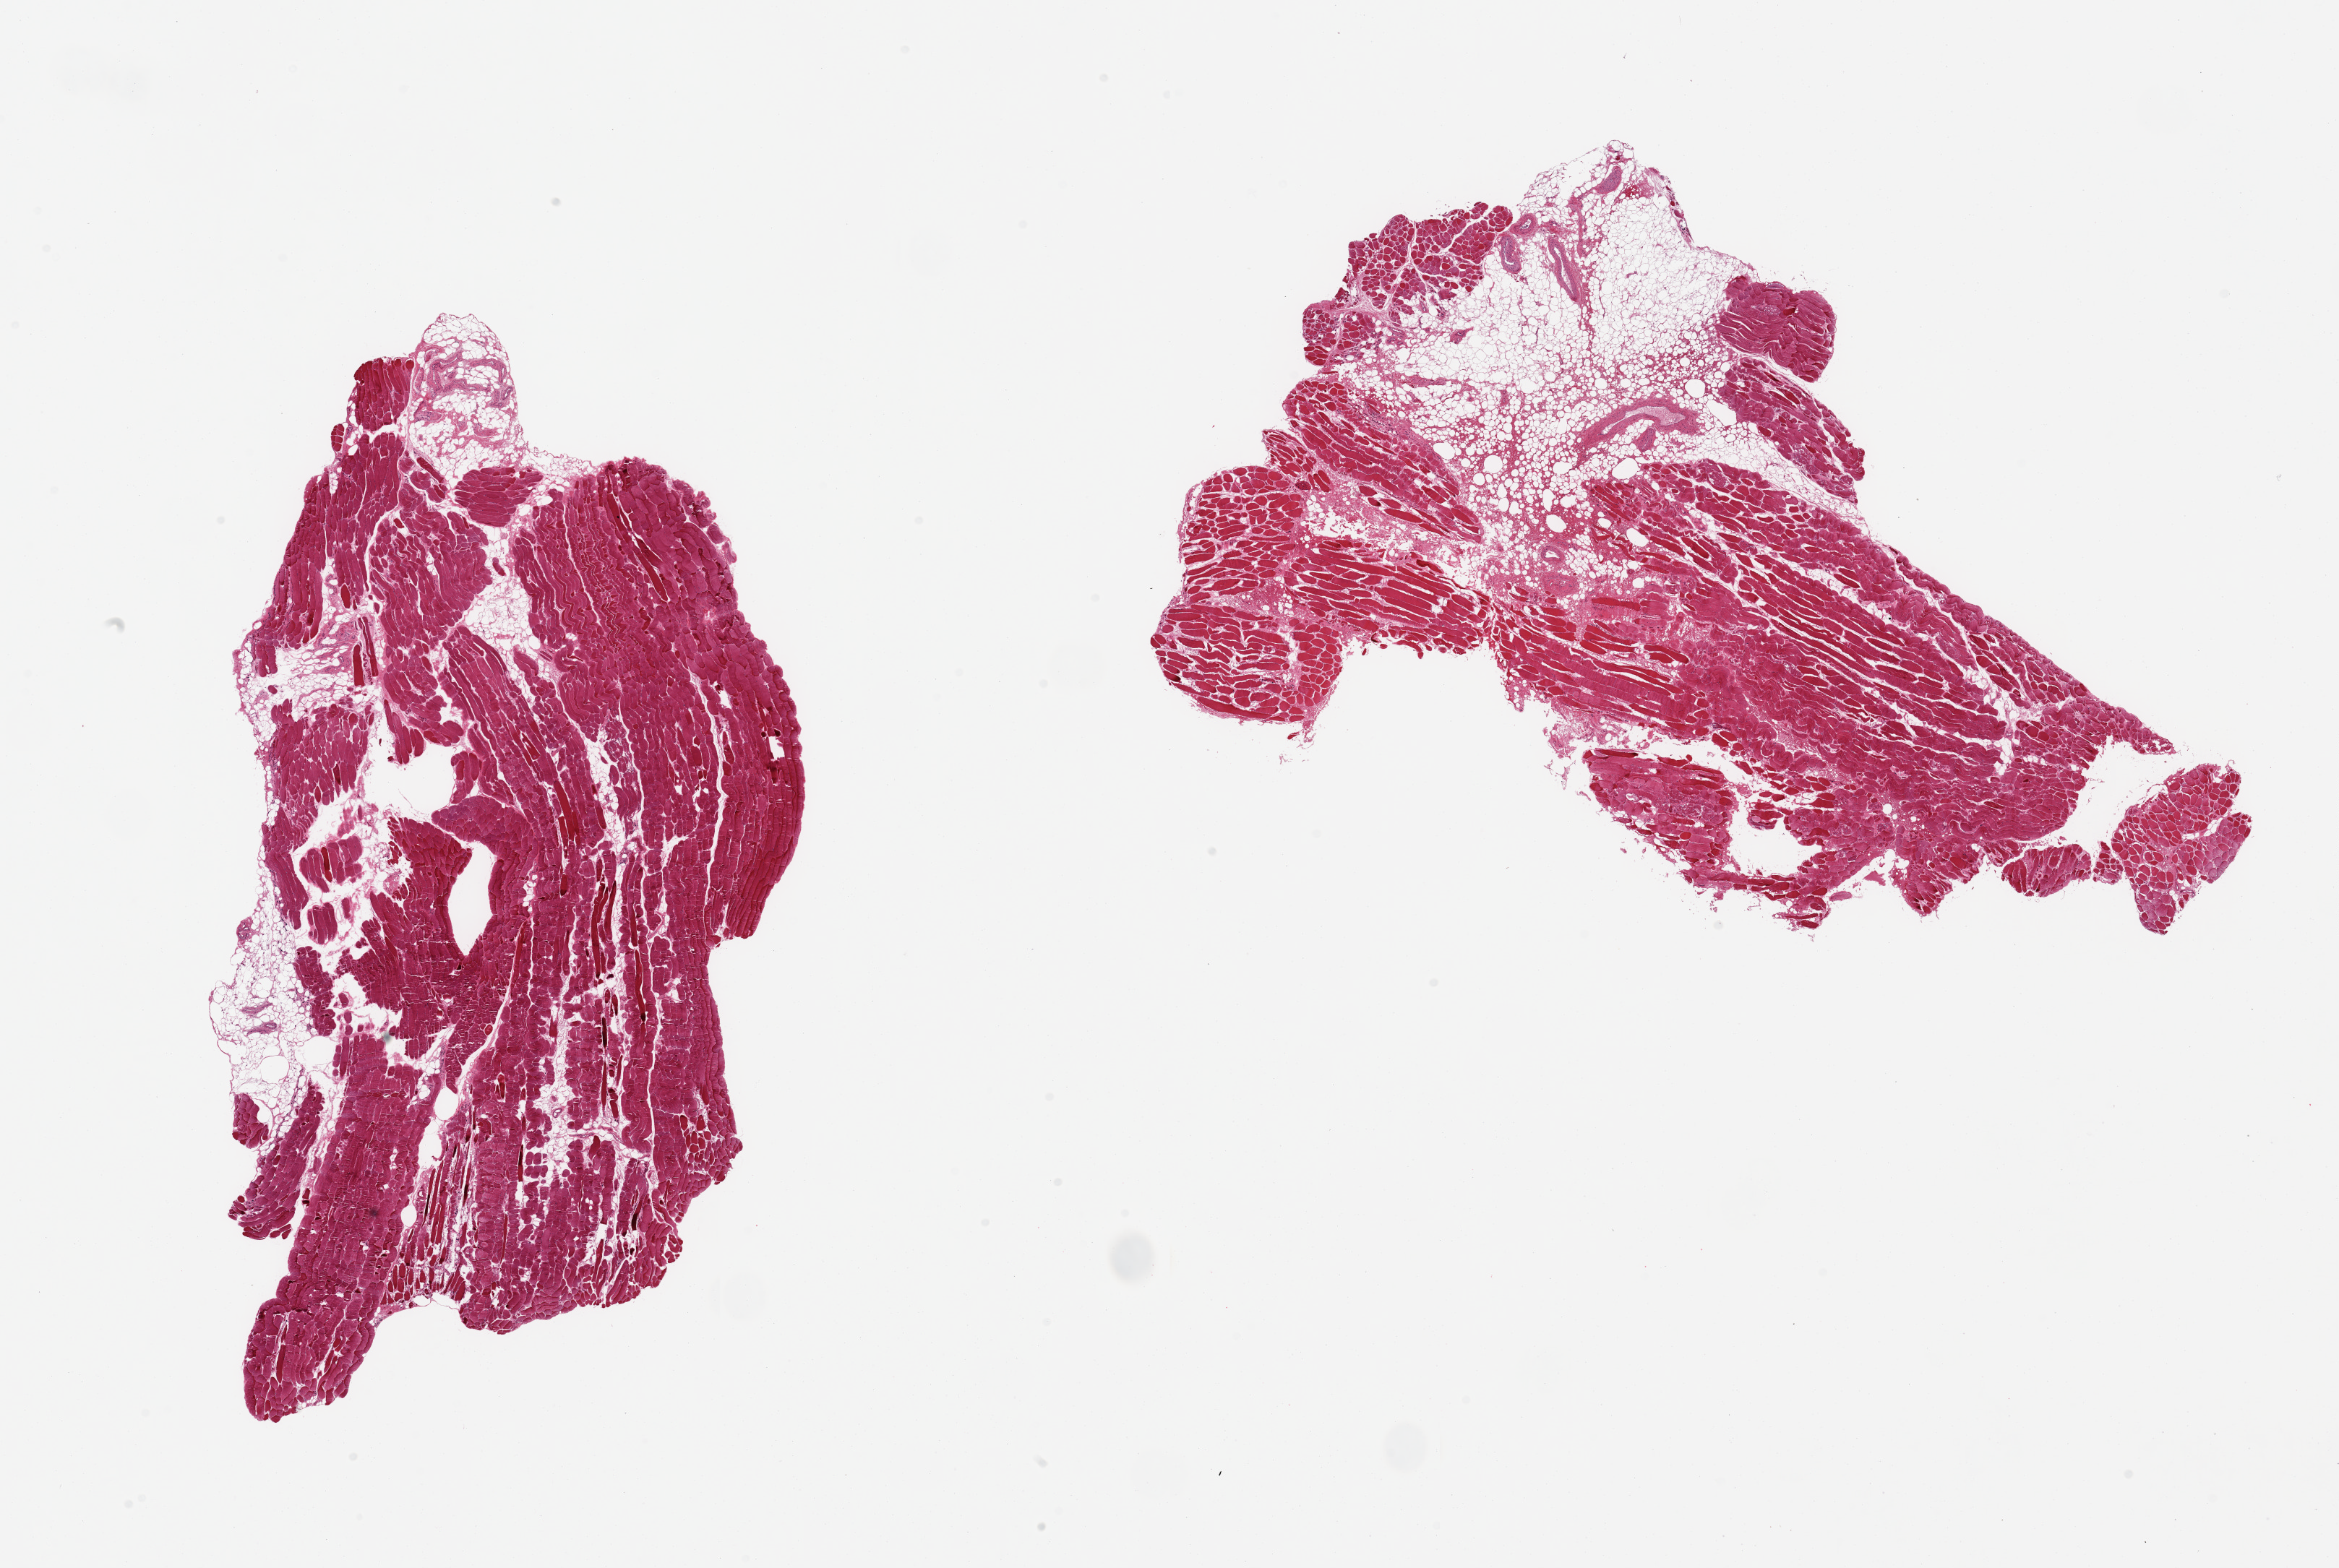
Hematoxylin and eosin (H&E) whole-slide image, brightfield — shown as a low-resolution overview of the whole scanned area (about 25.6 x 17.2 mm, slide scanned at 20x), PAXgene-fixed paraffin-embedded (PFPE) section, sampled site (target tissue): skeletal muscle, tissue donor sample. Donor: male.
Review note (as recorded): 2 pieces, ~30% interstitial or adherent fat/vascular elements.